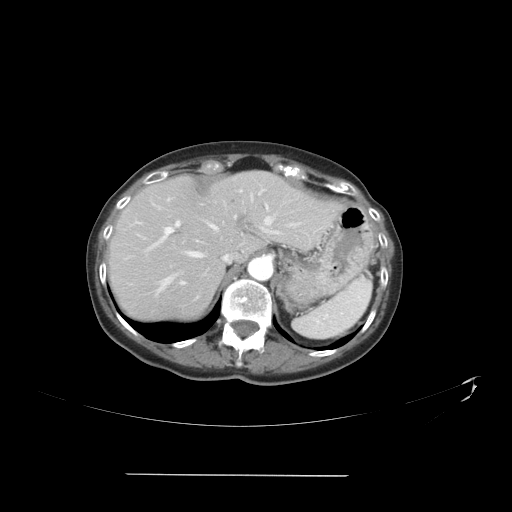
Contrast-enhanced abdominal CT, one axial slice; position 29 of 41 along the scan axis; reconstruction kernel STANDARD; soft-tissue window (W 400 / L 40 HU); 5 mm slice thickness; 512 × 512 image matrix, field of view 431 × 431 mm. Female patient, age 74 years. Case-level facts recorded for this patient, not image findings: diagnosis: colorectal cancer liver metastases, imaged before liver resection; multiple liver metastases: yes.
Outlined on this slice (manually delineated by an expert):
- hepatic veins: bounding box <151,192,278,293> (left, top, right, bottom; pixels)
- liver: <107,172,340,321>
- planned liver remnant (the part of the liver to remain after resection): <113,172,321,260>
- portal vein (with intrahepatic branches): <158,191,268,284>